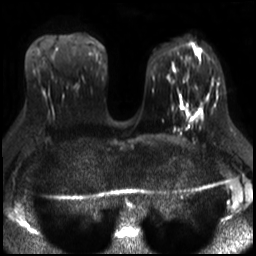
Breast MRI, one axial slice. Slice 15 of 30 in the series (ordered by position). Diffusion-weighted series; image 2 of 4 stored at this slice position (different b-values; order by instance number). 3 T. 4 mm slice thickness. 256 × 256 image matrix, field of view 320 × 320 mm. Female patient.
Annotated regions visible in this slice (outlined manually by an expert reader):
- tumour on diffusion-weighted imaging: box from (x=194, y=112) to (x=200, y=118) px